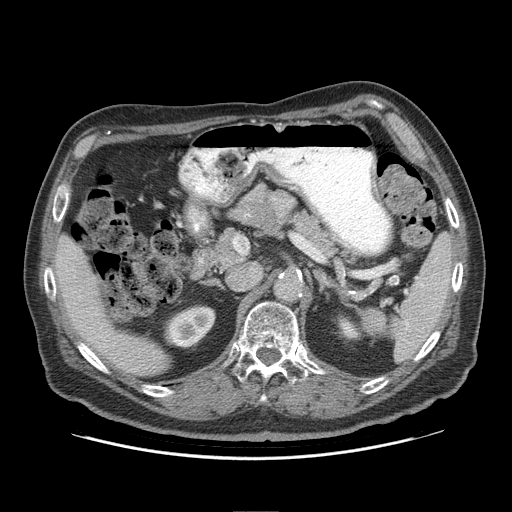
Contrast-enhanced abdominal CT (liver protocol), one axial slice. Position 51 of 95 along the scan axis. 140 kVp. Soft-tissue window (W 400 / L 40 HU). 2.5 mm slice thickness. 512 × 512 image matrix, field of view 400 × 400 mm. From the clinical record (not read from this slice): diagnosis: hepatocellular carcinoma (patient treated with transarterial chemoembolisation; whether this scan precedes or follows treatment is not stated here); TNM stage (as recorded): Stage-IVB; Child-Pugh class: A; tumour nodularity: uninodular.
Annotated regions visible in this slice (semi-automatically segmented with operator editing):
- liver parenchyma outside the tumour (the mass and vessels are separate outlines, so this box may not span the whole liver): bounding box [x1, y1, x2, y2] px = [54, 234, 168, 375]